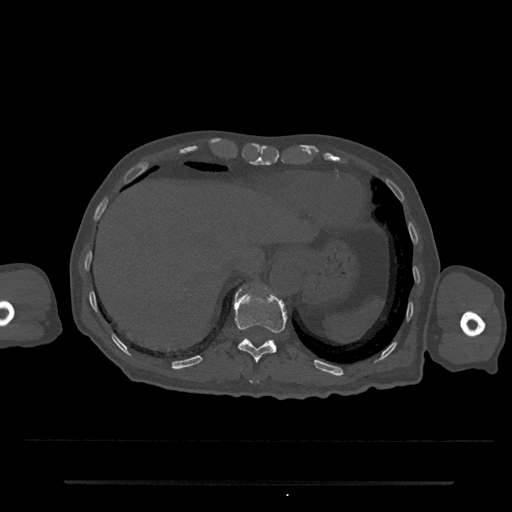
CT including the spine, one axial slice. Position 250 of 797 along the scan axis. 120 kVp. Bone window (W 1800 / L 400 HU). 0.5 mm slice thickness. 512 × 512 image matrix, field of view 427 × 427 mm. Patient: male, 74 years. From the clinical record (not read from this slice): primary cancer: prostate.
Annotated regions visible in this slice (semi-automatic segmentation, software-assisted and operator-edited):
- T10 vertebra: box from (x=250, y=378) to (x=259, y=384) px
- T11 vertebra: (x=234, y=289)–(x=287, y=362)